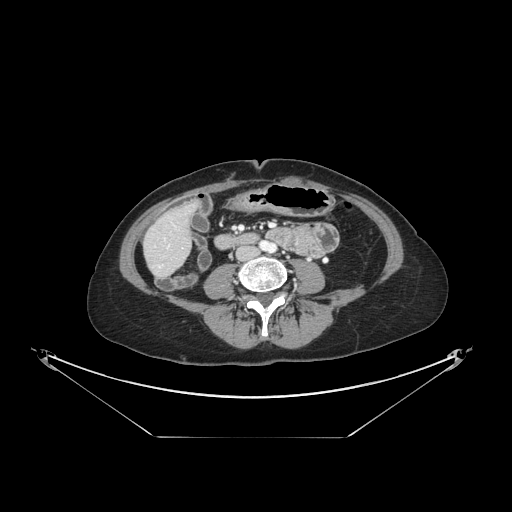
Contrast-enhanced abdominal CT, one axial slice. Slice 30 of 148 in the series (ordered by position). Reconstruction kernel STANDARD. Intravenous contrast given. Soft-tissue window (W 400 / L 40 HU). 2.5 mm slice thickness. 512 × 512 image matrix. Female patient, age 73 years. Case-level facts recorded for this patient, not image findings: diagnosis: colorectal cancer liver metastases, imaged before liver resection; multiple liver metastases: no; largest metastasis: 1 cm; disease in both lobes: no.
Outlined on this slice (outlined manually by an expert reader):
- hepatic veins: bounding box (x1, y1, x2, y2) in pixels: (167, 246, 169, 248)
- liver: (145, 207, 191, 276)
- planned liver remnant (the part of the liver to remain after resection): (163, 207, 191, 237)